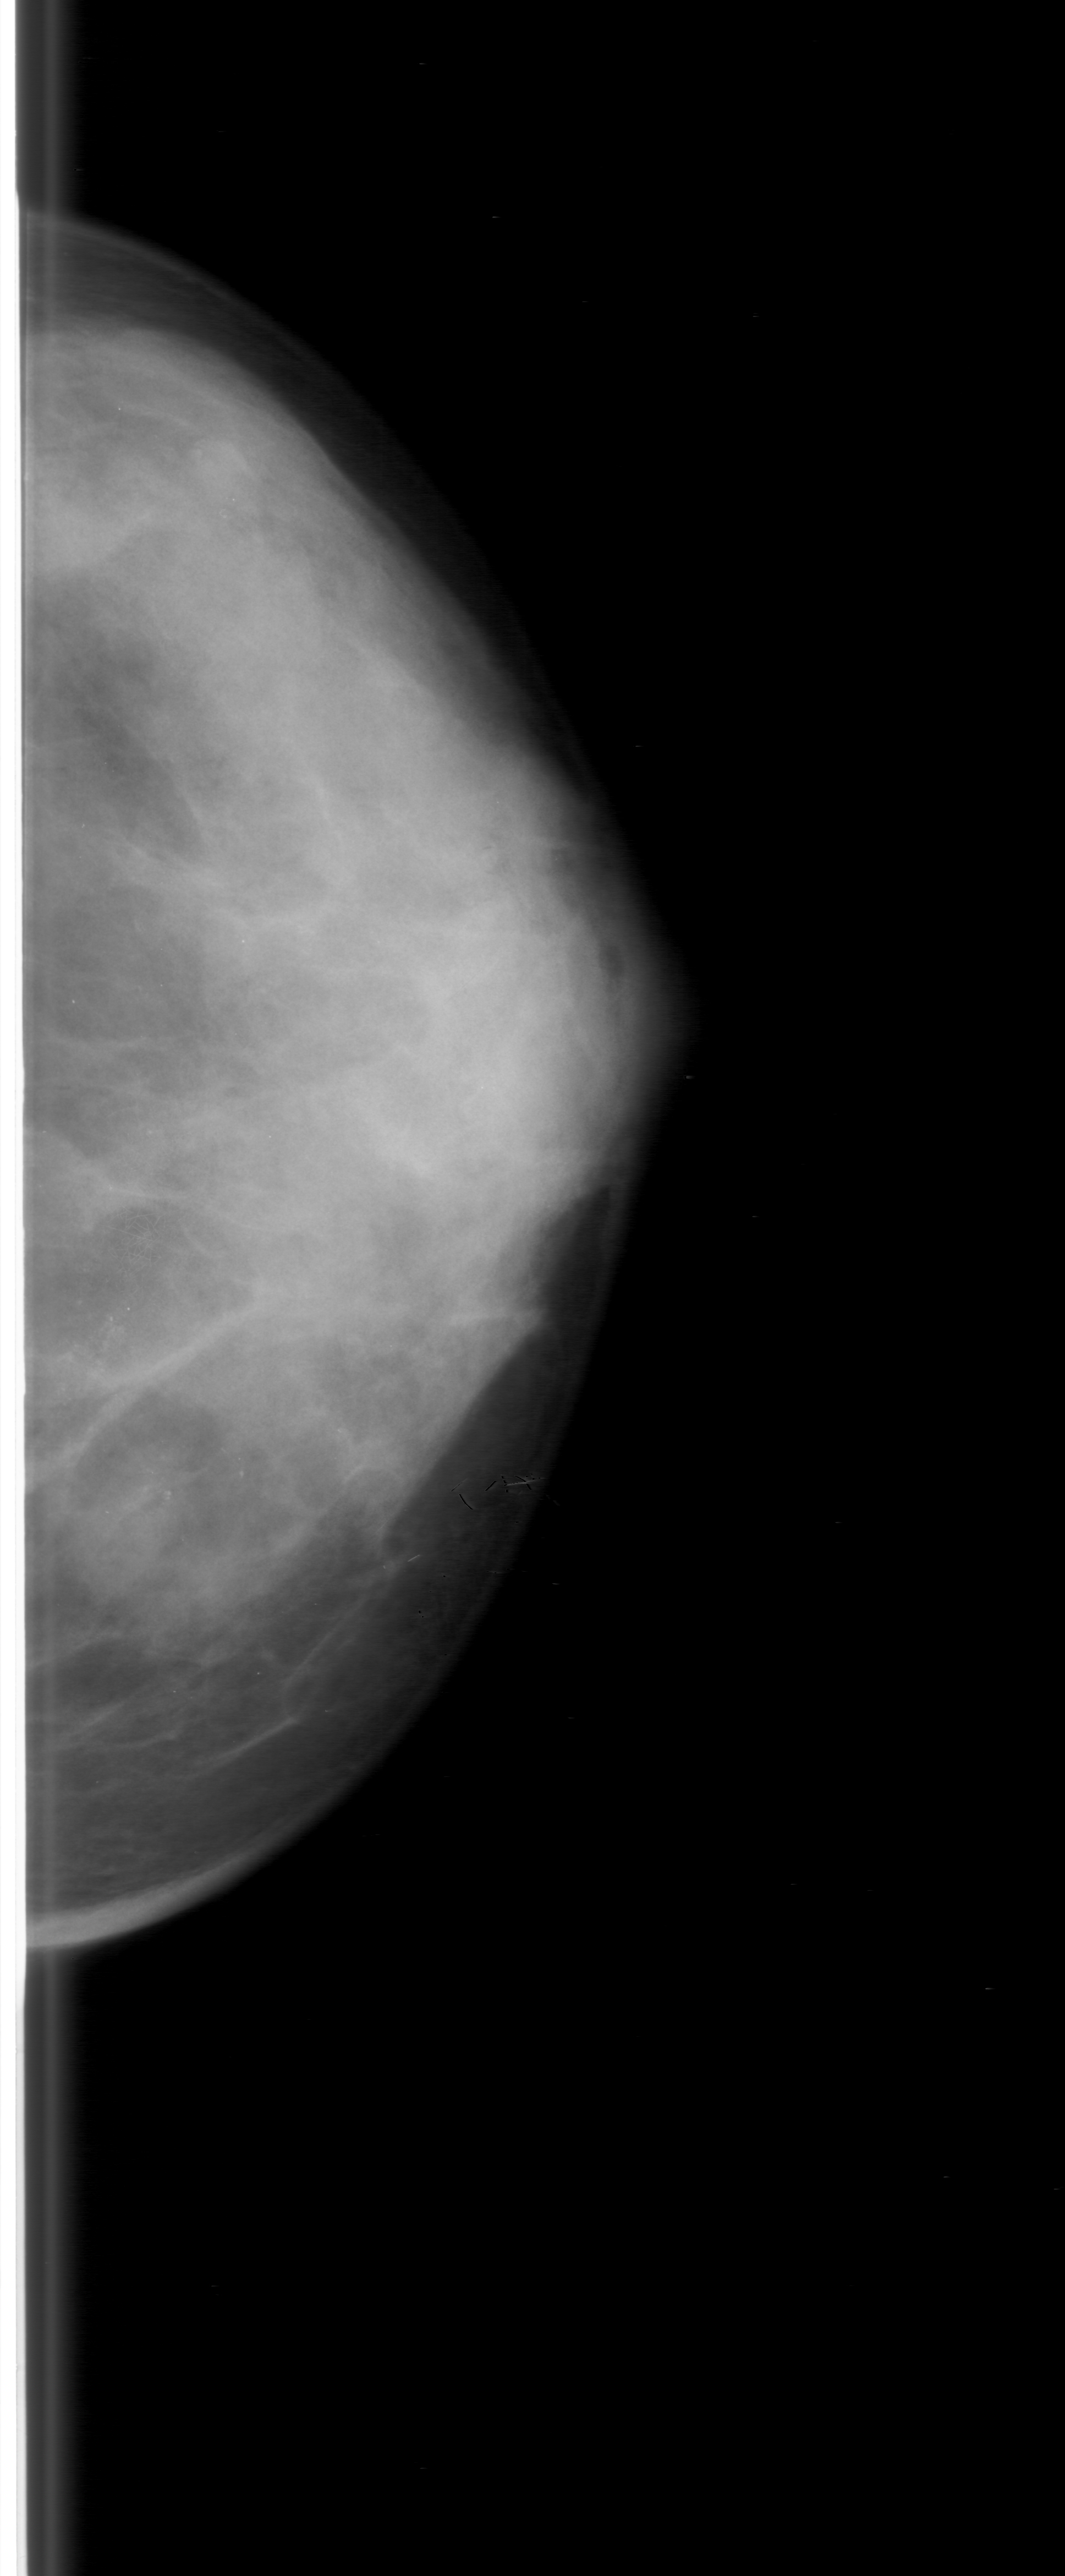
Mammogram (digitized film). Left breast. Craniocaudal (CC) view. Breast composition: heterogeneously dense (BI-RADS density category 3 of 4). 1065 × 2576 image matrix.
Expert-marked regions of interest on this film, with their recorded descriptors:
- calcifications, morphology fine linear branching, distribution linear; BI-RADS assessment category 3; pathology result (as recorded, not read from the image): malignant: bounding box <45,1031,383,1462> (left, top, right, bottom; pixels)